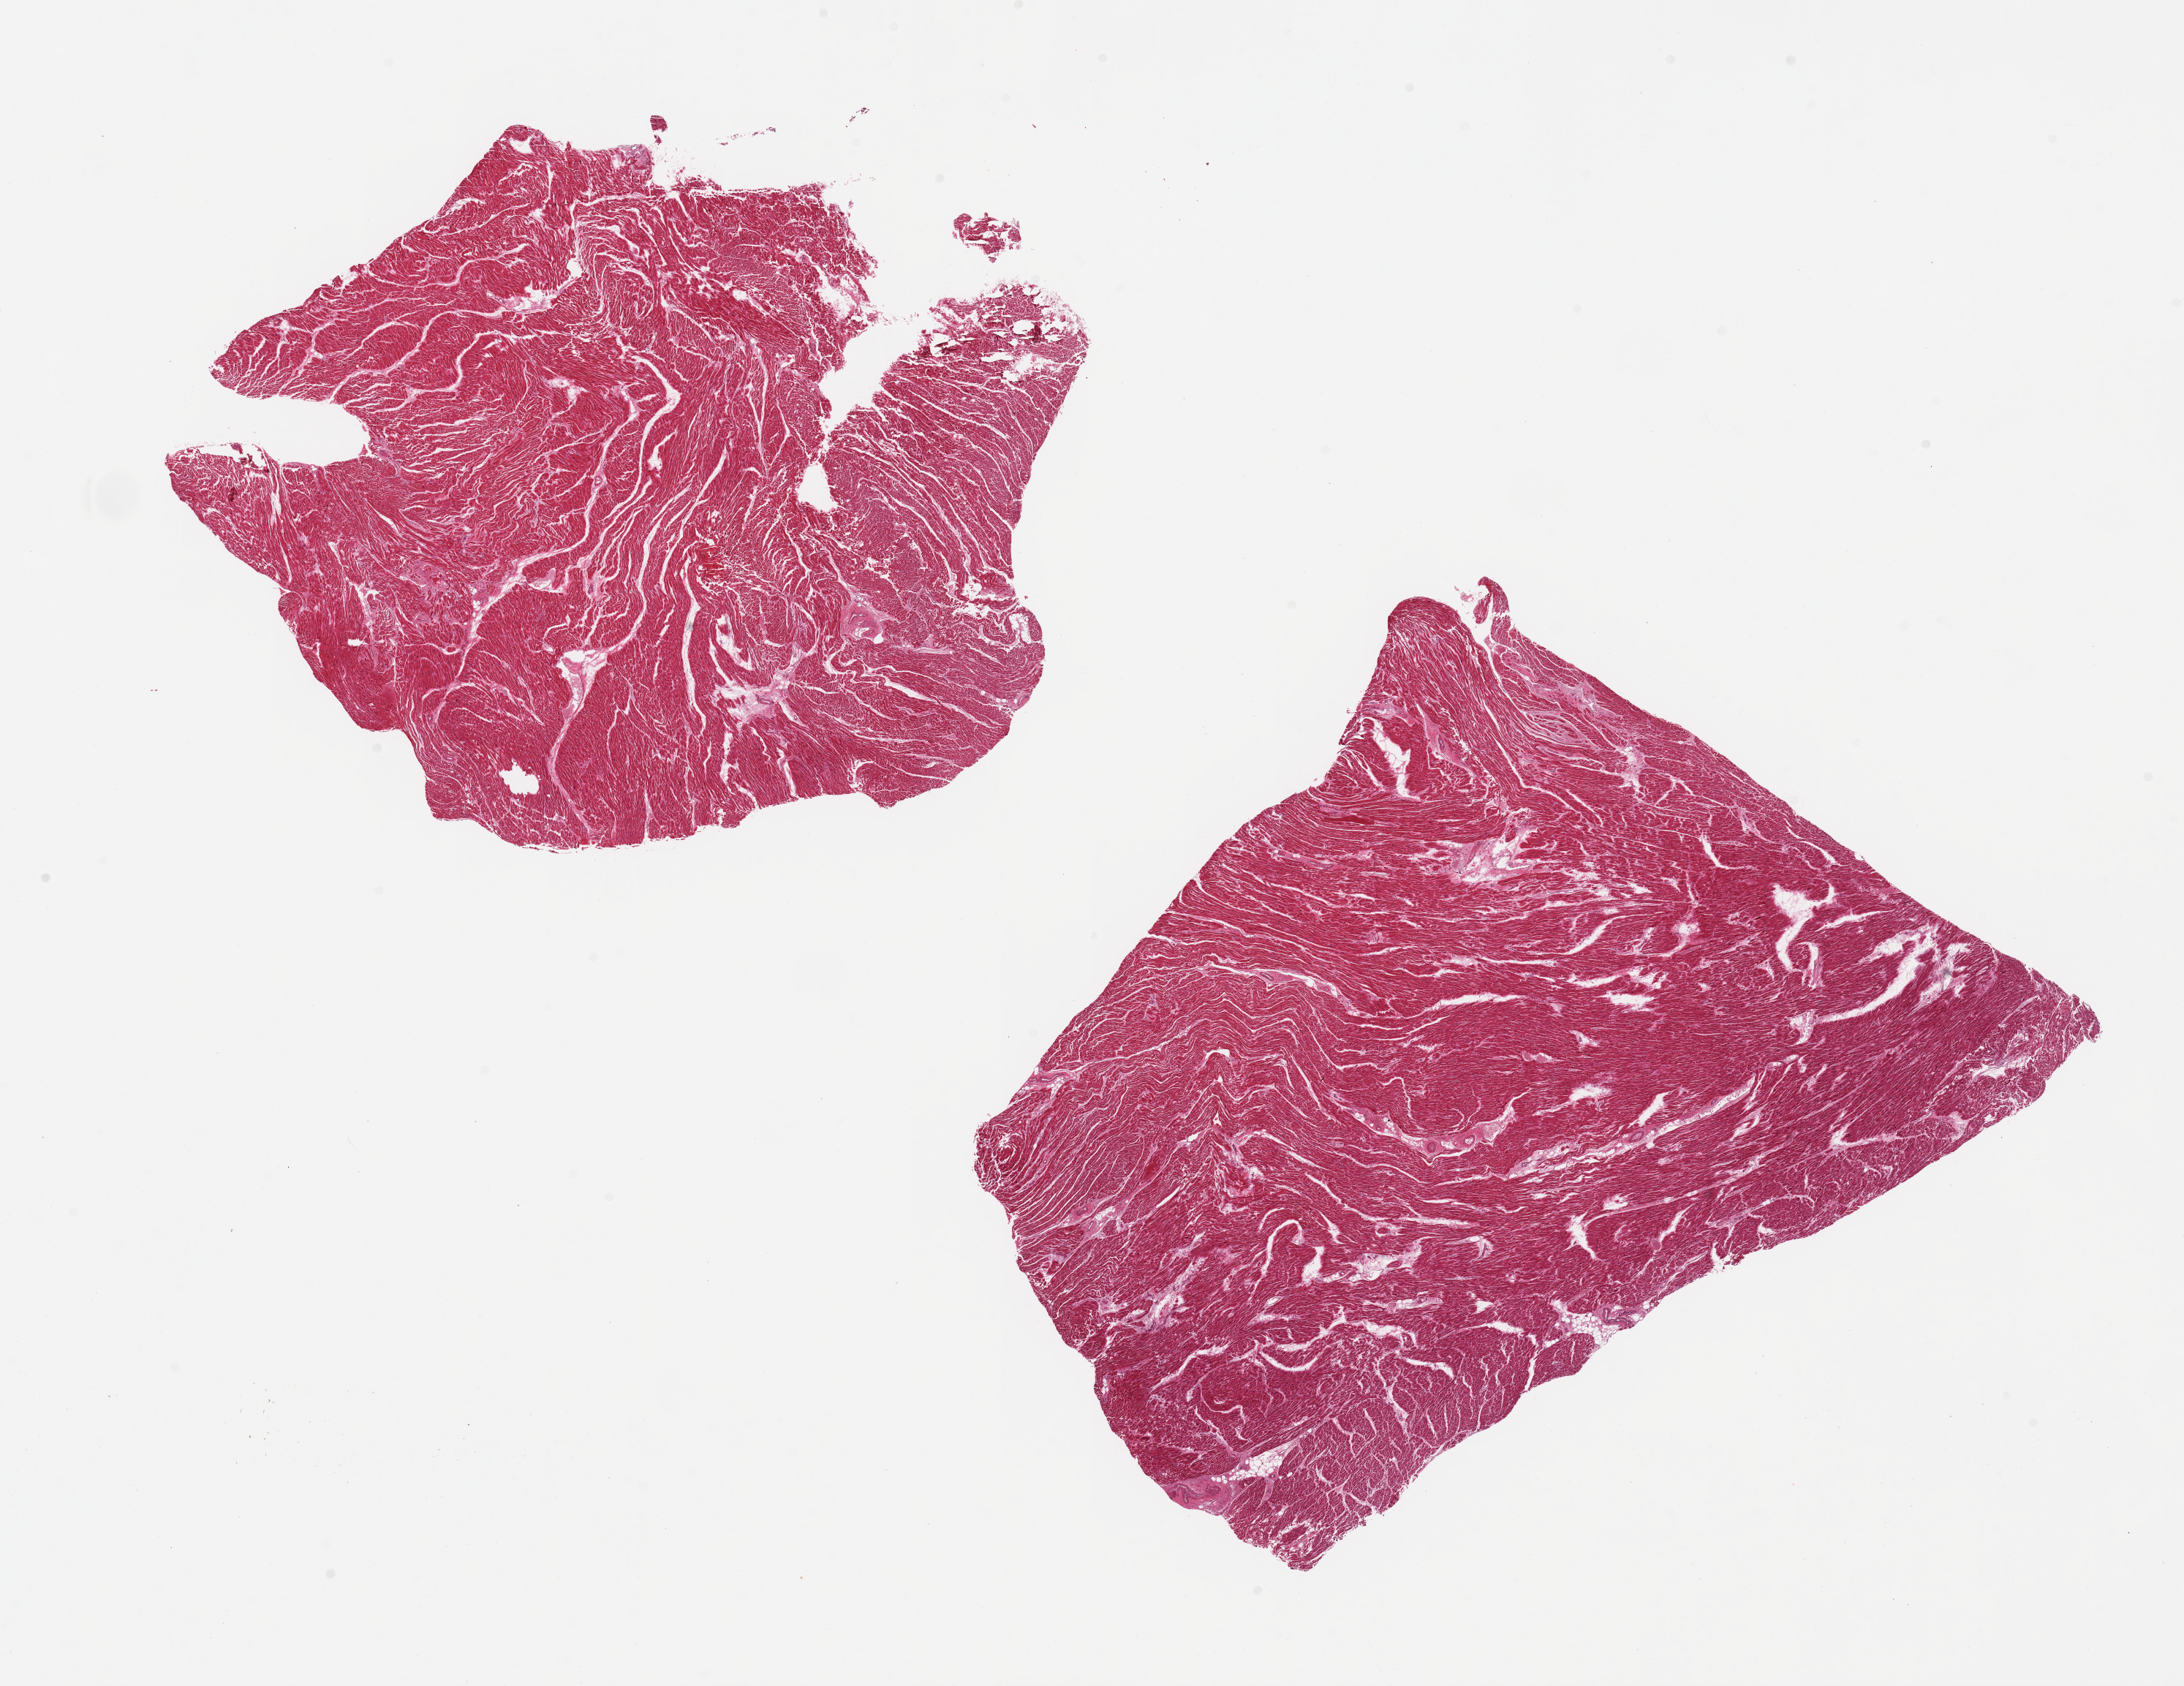
Digitized H&E-stained section, brightfield, whole scanned area (about 23.6 x 18.2 mm, from a 20x scan) shown as a low-resolution overview; PAXgene-fixed paraffin-embedded (PFPE) section; sampled site (target tissue): heart; tissue donor sample. Female donor.
Review note (as recorded): 2 pieces, slight interstitial fibrosis/chronic ischemic damage.